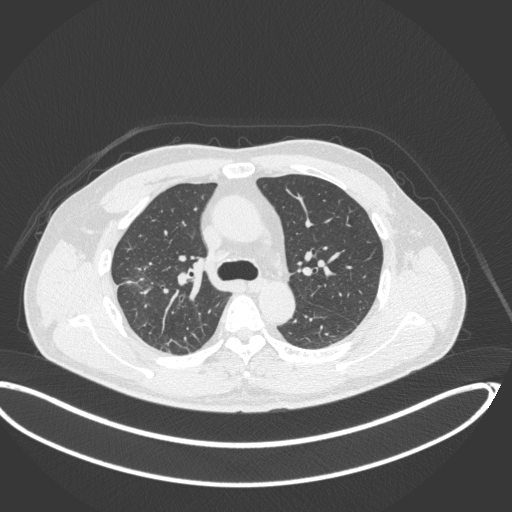
Chest CT, one axial slice. Reconstruction kernel B31f. Lung window (W 1500 / L -600 HU). 1 mm slice thickness. 512 × 512 image matrix, field of view 439 × 439 mm. Male patient, age 63 years. From the clinical record (not read from this slice): clinical TNM (as recorded): T1c N0 M0; histopathological grade: G2-3.
Structures marked on this image (bounding box drawn by a radiologist):
- lung tumour (recorded histology: adenocarcinoma): box from (x=126, y=259) to (x=159, y=300) px